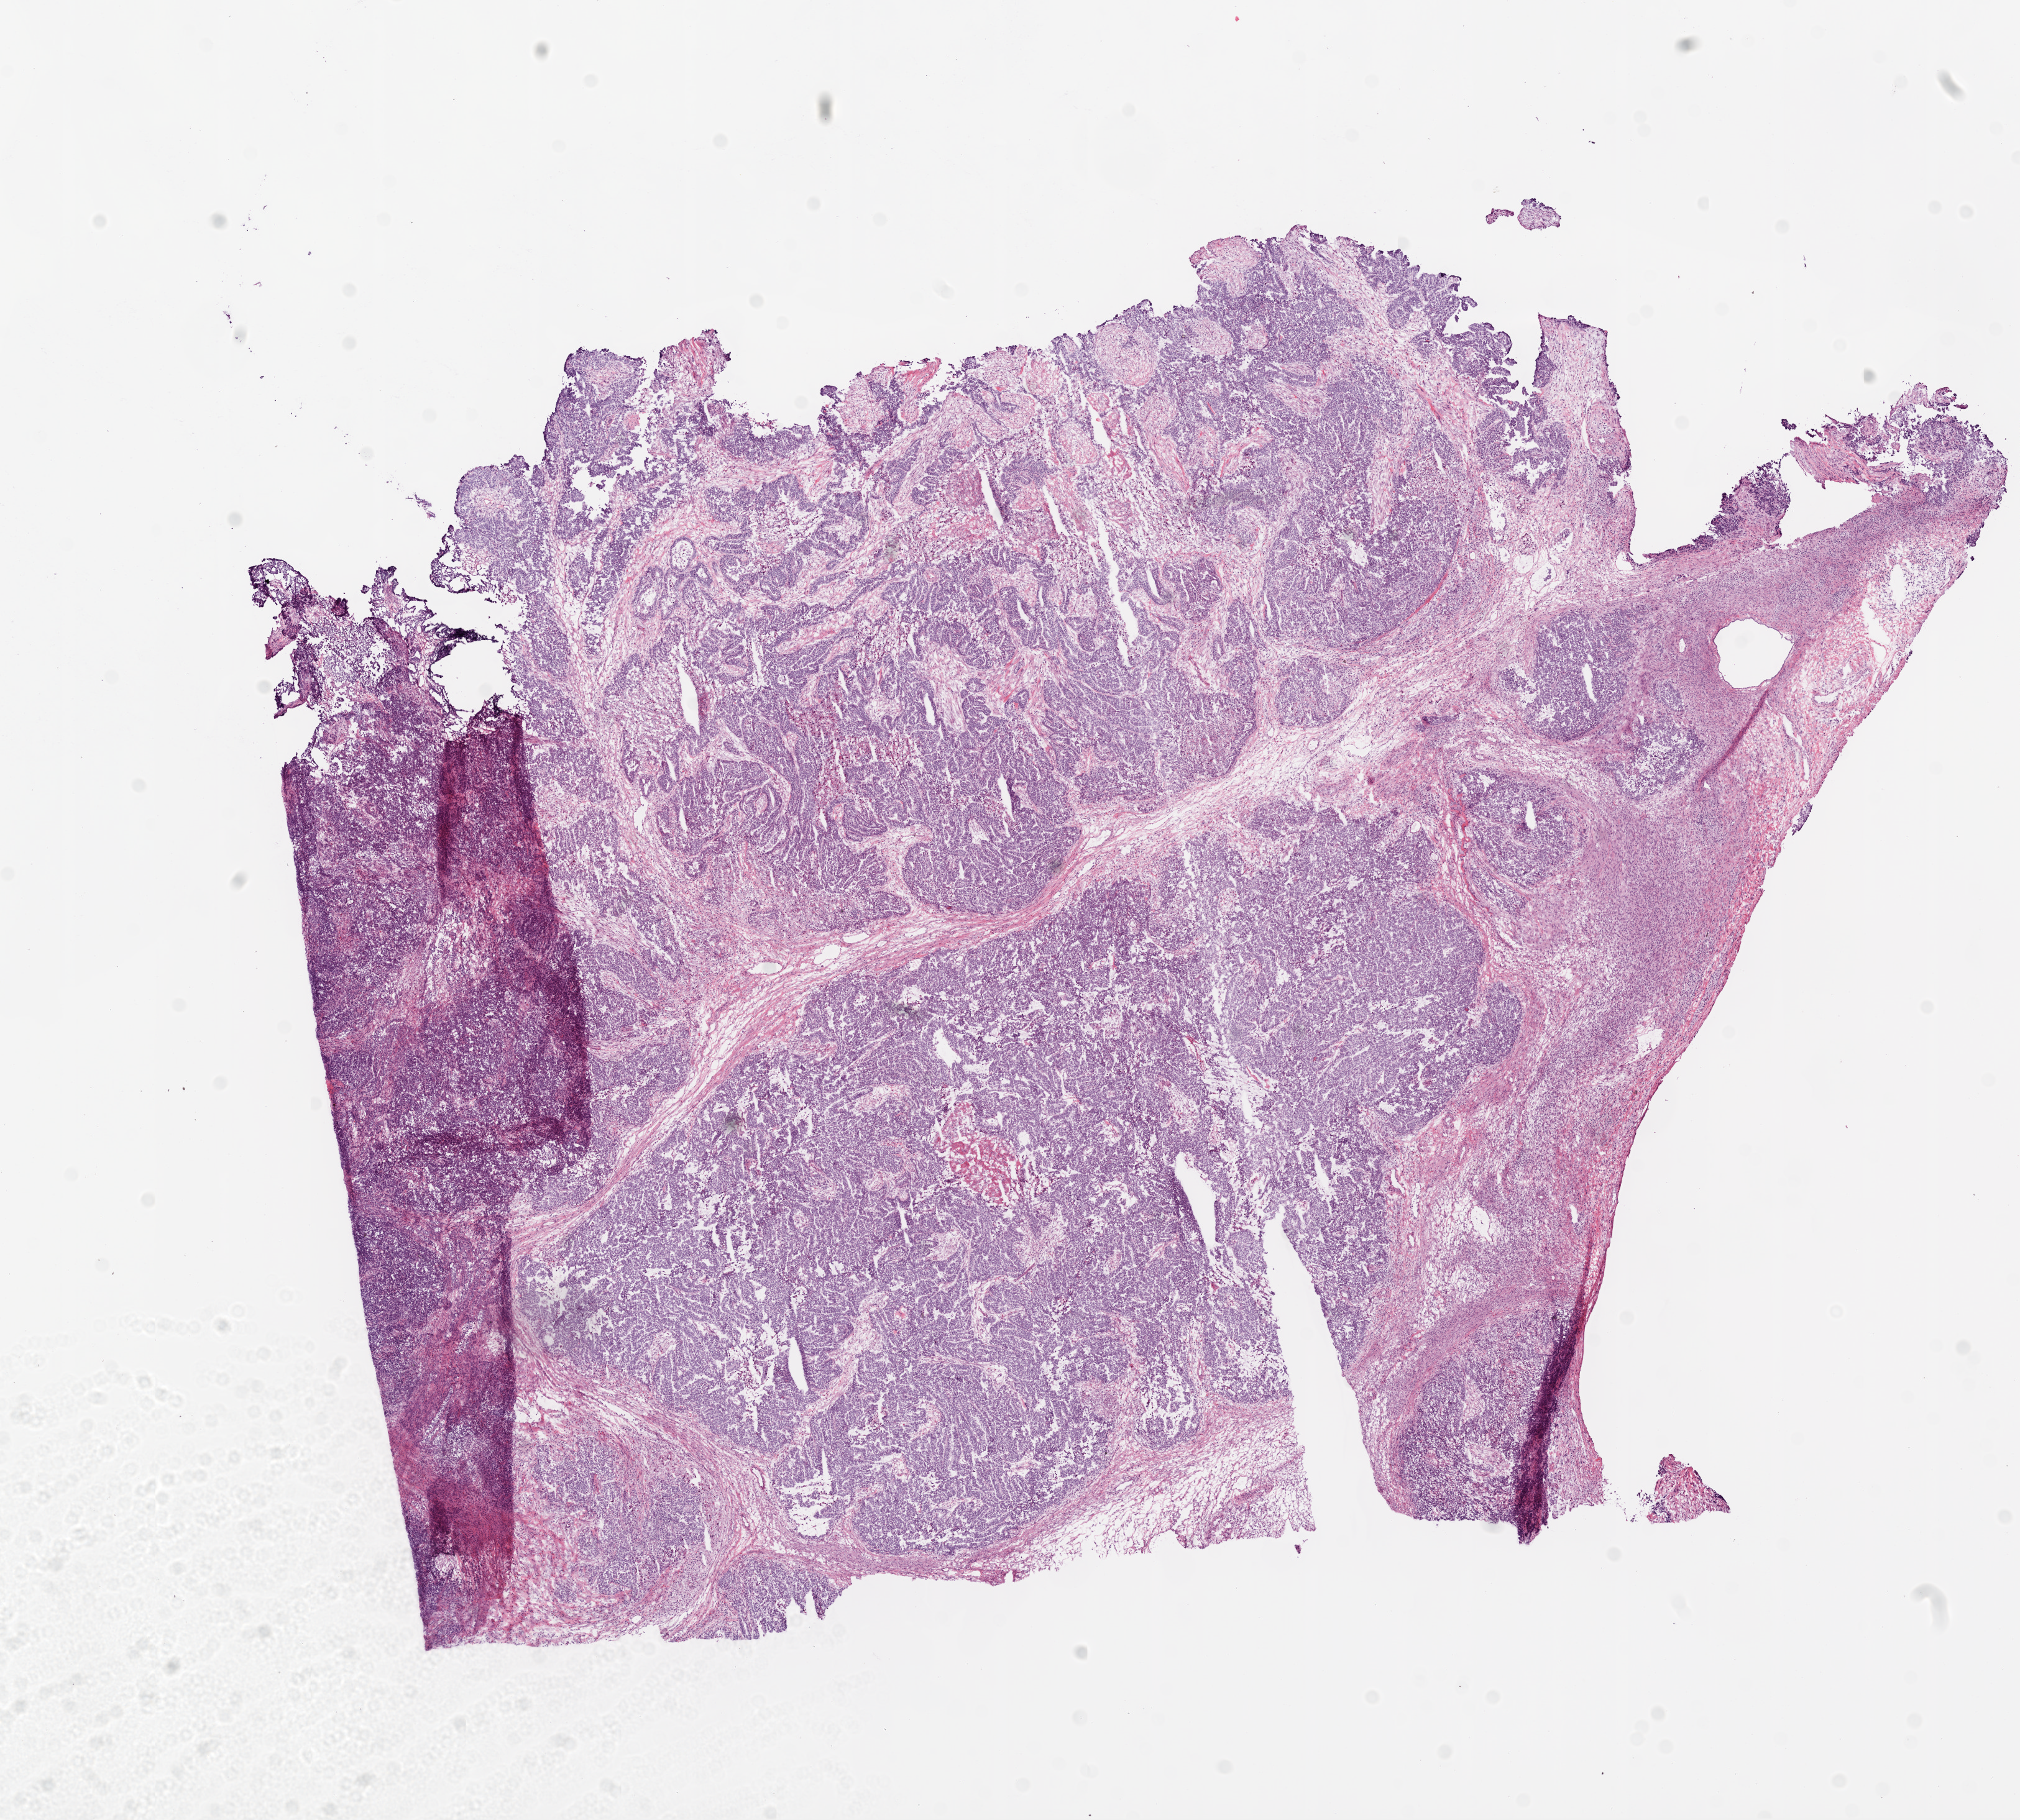
Whole-slide histology image, H&E-stained — low-resolution overview of the scanned area, about 13.0 x 11.8 mm (from a 20x scan), frozen section from the top of the tissue portion, primary tumour sample from the ovary. Female, age 80 years at initial diagnosis. Histologic grade: G3 (poorly differentiated). Slide review estimates, as recorded: tumour cells 80%, tumour nuclei 85%, normal cells 1%, stromal cells 14%, necrosis 5%.
* laterality: left
* histologic diagnosis: Serous cystadenocarcinoma, NOS
* FIGO stage: IIIC